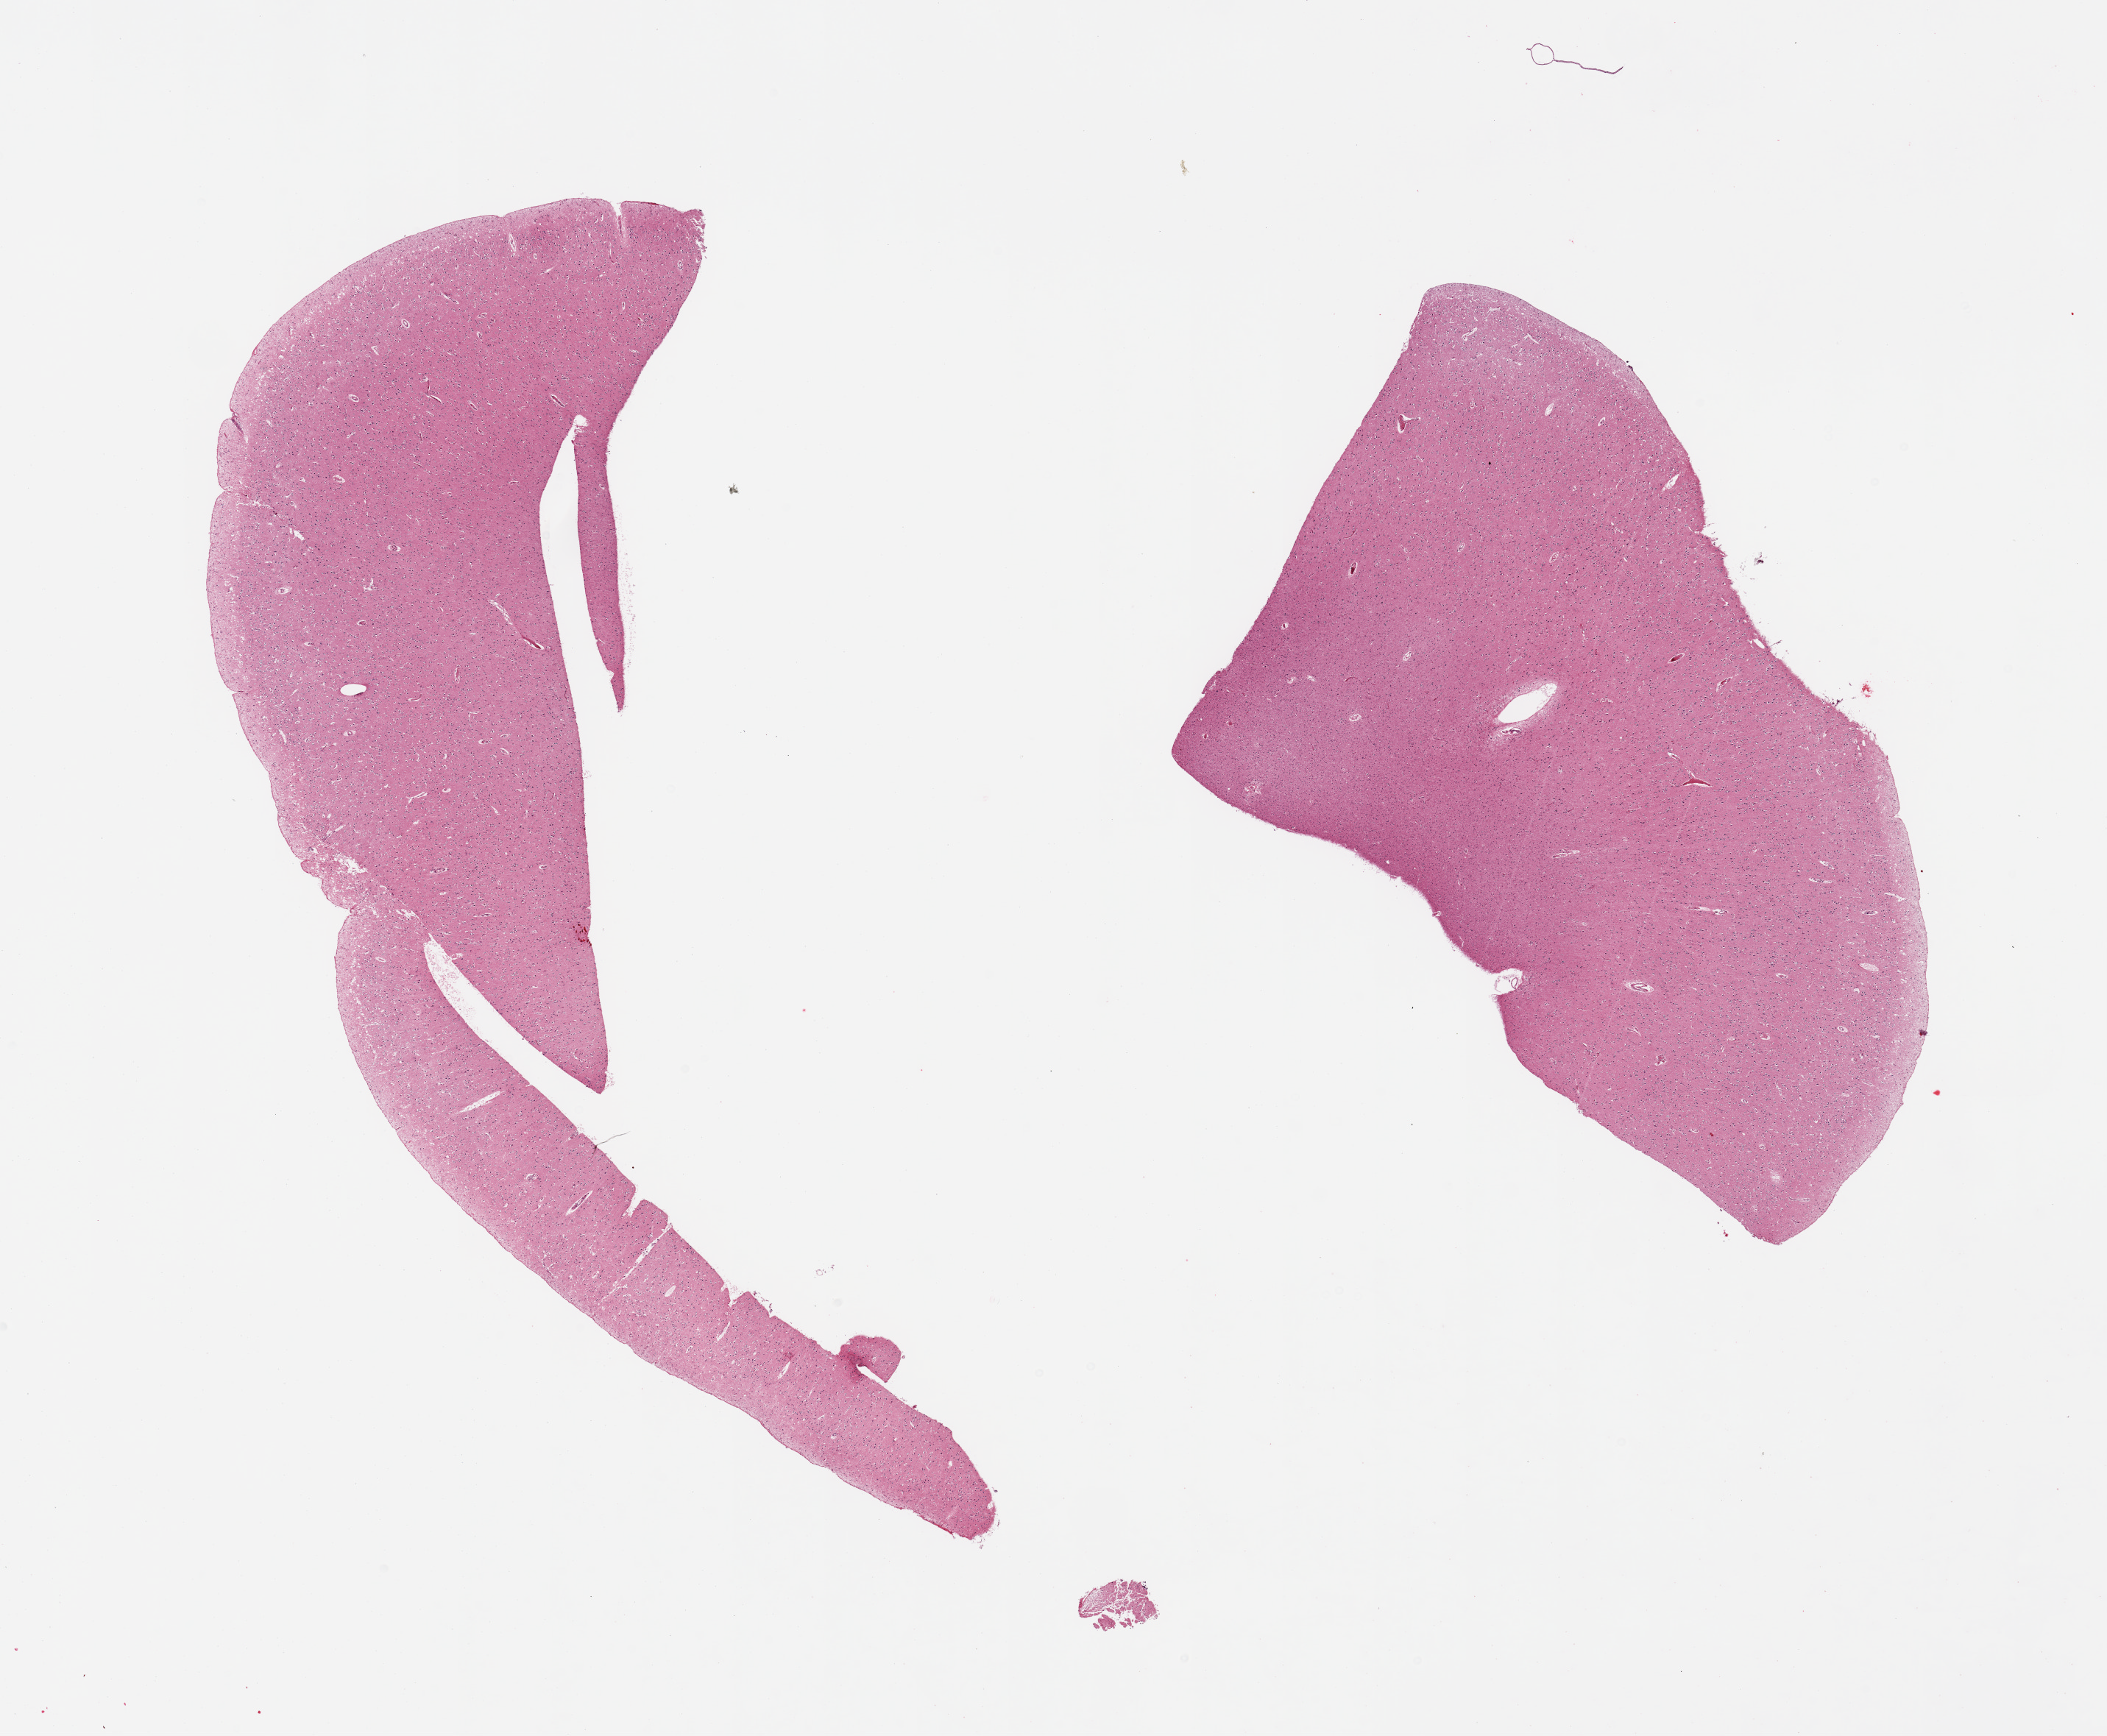
Digitized haematoxylin and eosin-stained section, low-resolution overview of the scanned area, about 22.6 x 18.7 mm (acquisition: 20x scan); PAXgene-fixed, paraffin-embedded tissue; sampled site (target tissue): cerebral cortex; tissue donor sample. Donor sex: male.
Pathologist's review note for this sample: 2 pieces.